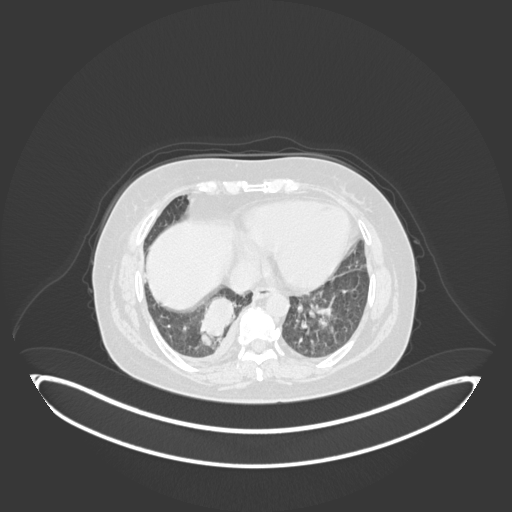
Chest CT, one axial slice; slice 43 of 231 in the series (ordered by position); 120 kVp; lung window (W 1500 / L -600 HU); 1 mm slice thickness; 512 × 512 image matrix, field of view 500 × 500 mm. Patient: female, 56 years. Case-level facts recorded for this patient, not image findings: clinical TNM (as recorded): T2b N1 M0.
Structures marked on this image (rectangle marked by the reading radiologist):
- lung tumour (recorded histology: small cell carcinoma): box from (x=194, y=293) to (x=239, y=350) px